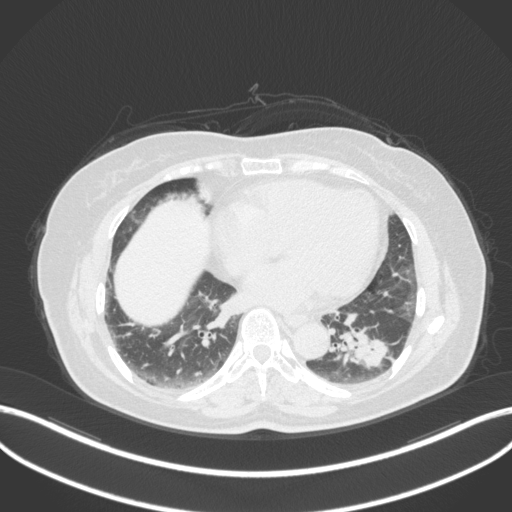
Chest CT, one axial slice. Position 143 of 307 along the scan axis. 120 kVp. Lung window (W 1500 / L -600 HU). 1 mm slice thickness. 512 × 512 image matrix, field of view 400 × 400 mm. Female patient, age 59 years. Case-level facts recorded for this patient, not image findings: clinical TNM (as recorded): T2a N0 M0; histopathological grade: G2-3.
Structures marked on this image (rectangle marked by the reading radiologist):
- lung tumour (recorded histology: adenocarcinoma): bounding box [x1, y1, x2, y2] px = [326, 311, 393, 371]